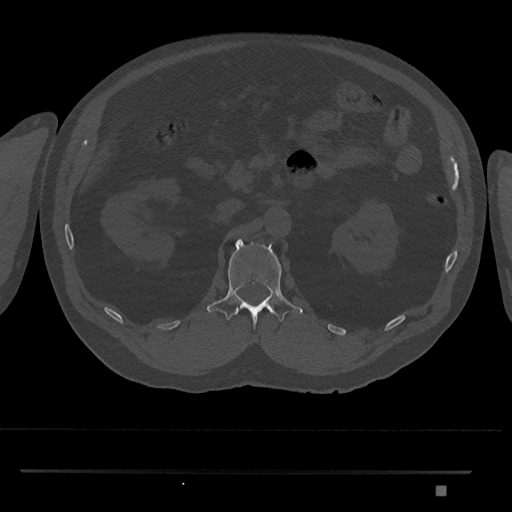
CT including the spine, one axial slice. Slice 824 of 1134 in the series (ordered by position). Reconstruction kernel Br40s/3. 120 kVp. Bone window (W 1800 / L 400 HU). 512 × 512 image matrix, field of view 429 × 429 mm. Patient: male, 65 years. Case-level facts recorded for this patient, not image findings: primary cancer: prostate.
Outlined on this slice (semi-automatically segmented with operator editing):
- L1 vertebra: bounding box [x1, y1, x2, y2] px = [207, 239, 303, 328]